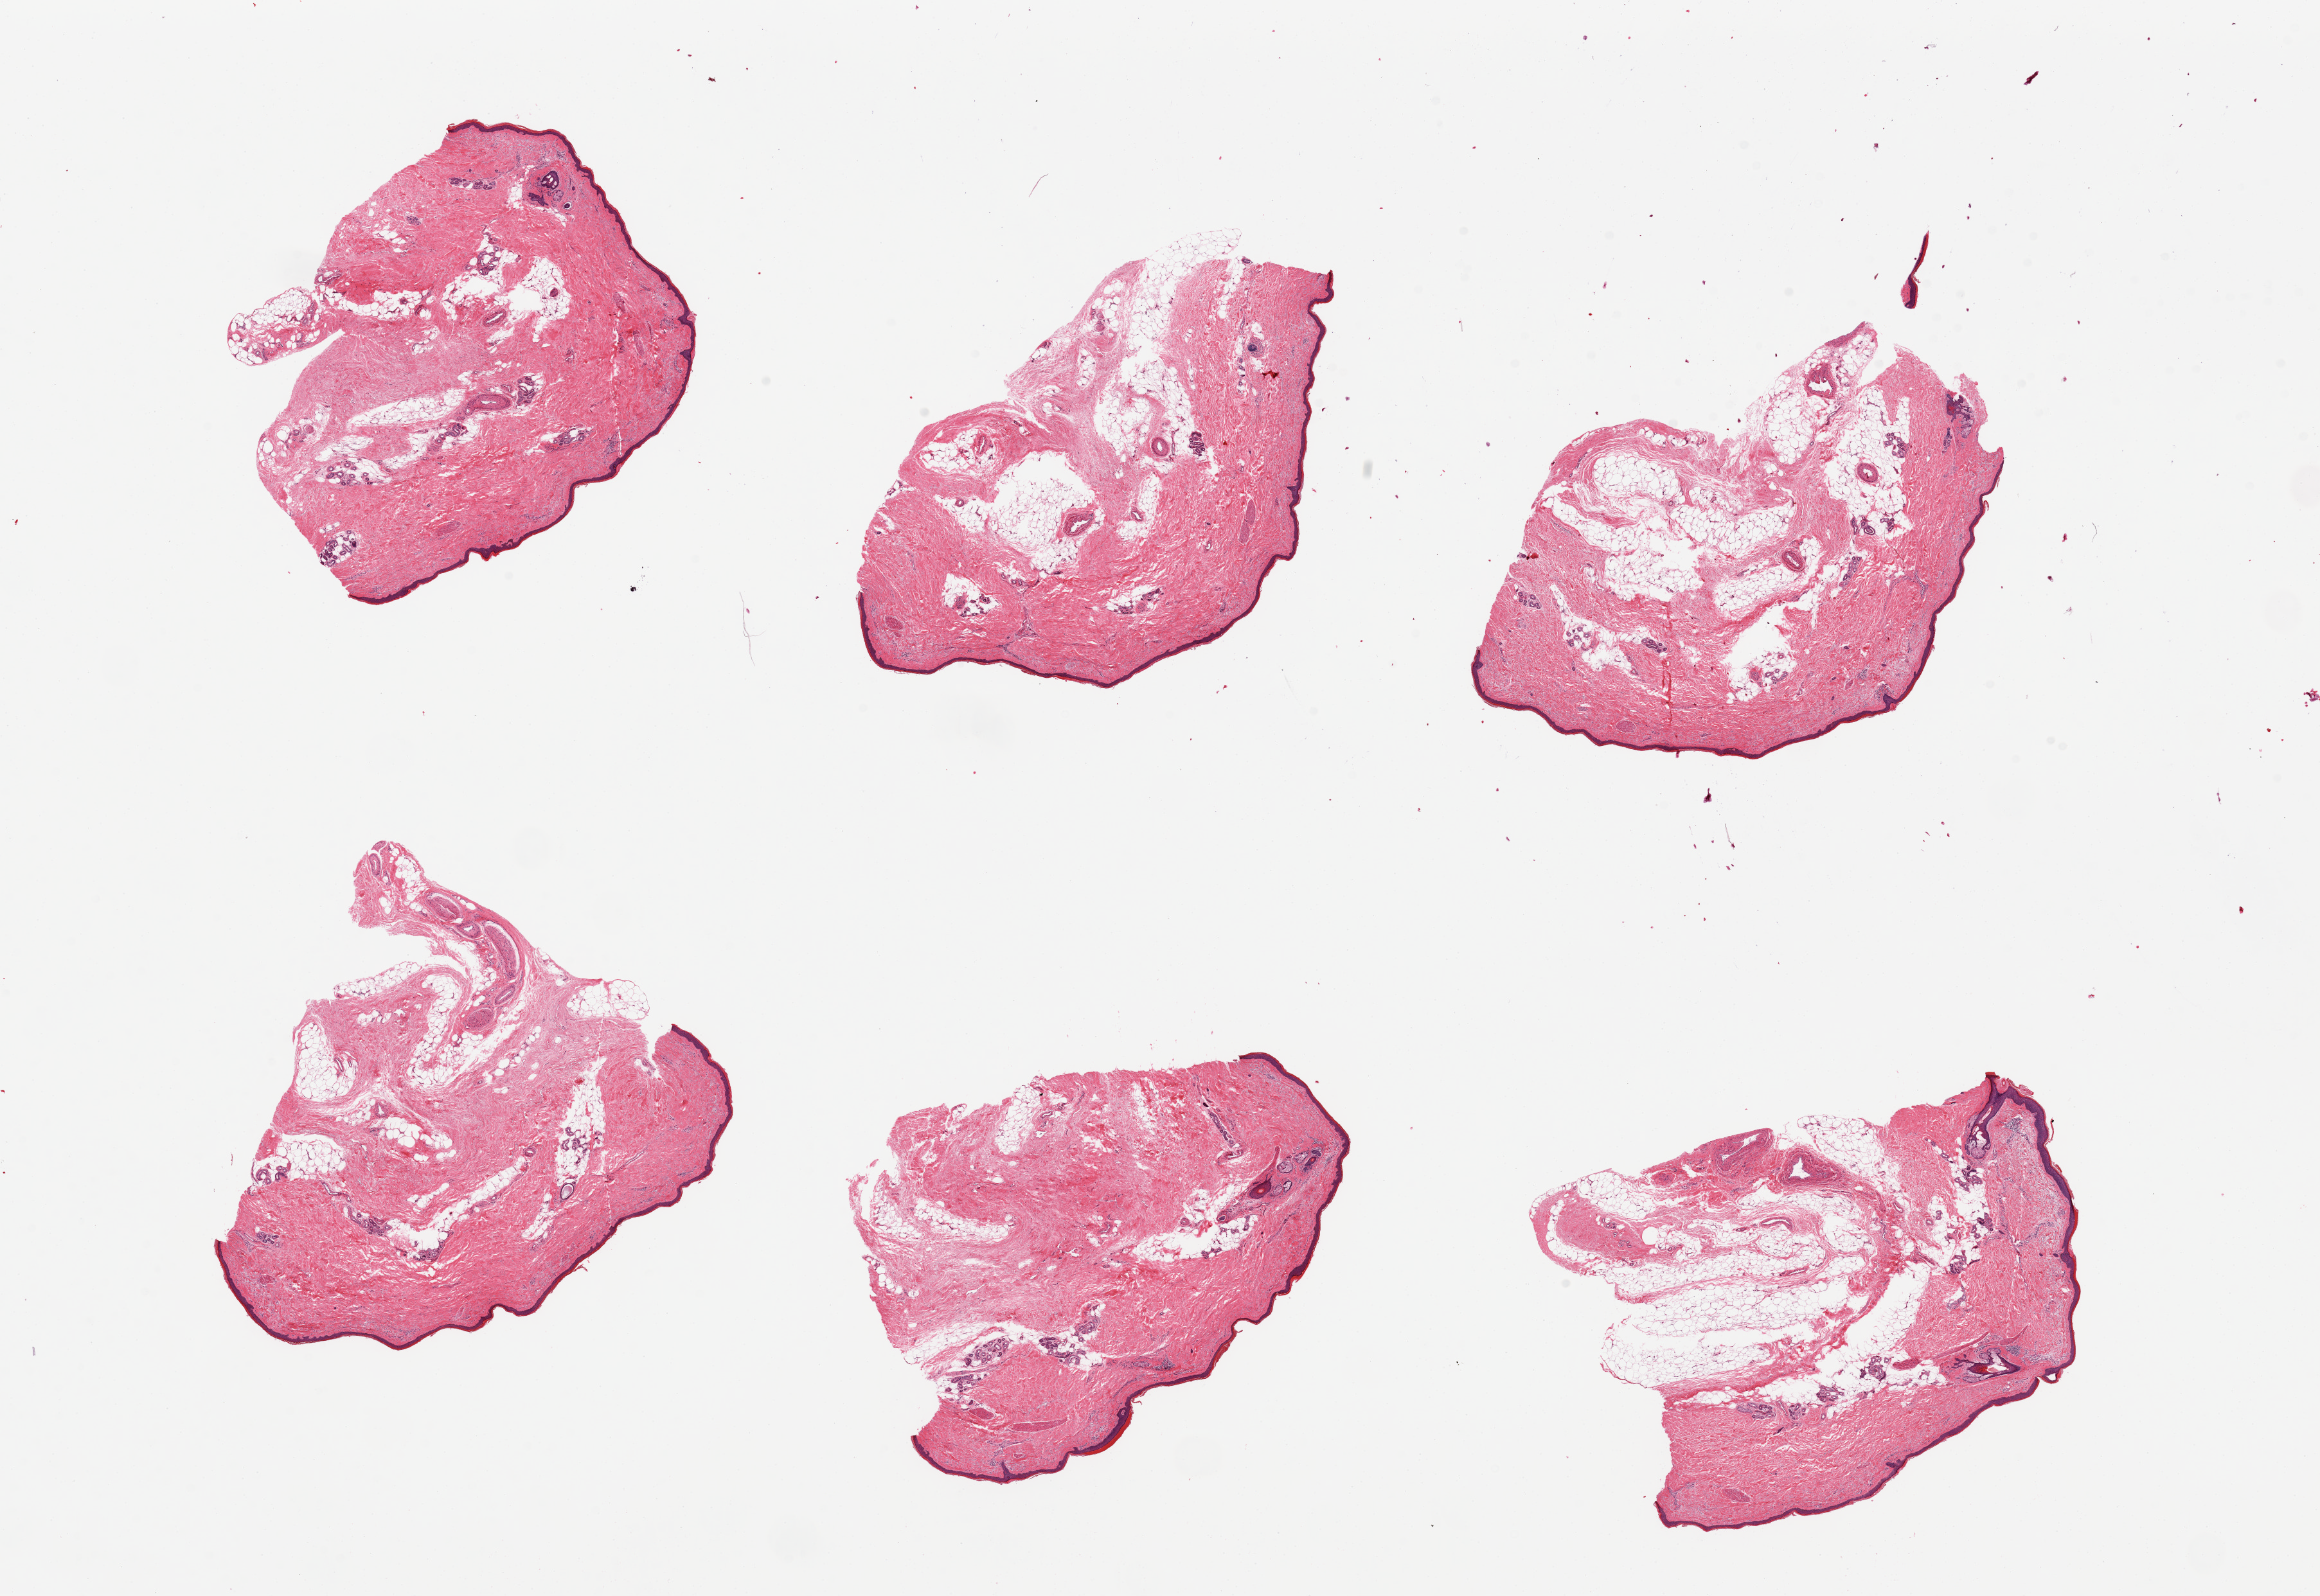
Whole-slide image, haematoxylin and eosin stain — whole scanned area (about 28.5 x 19.6 mm, slide scanned at 20x) shown as a low-resolution overview, PAXgene-fixed paraffin-embedded (PFPE) section, section of skin of lower leg (target tissue), tissue donor sample. Donor sex: male.
- review note (as recorded): 6 pieces, include internal and attached adipose tissue up to 40%, squamous epithelium measures ~40 microns